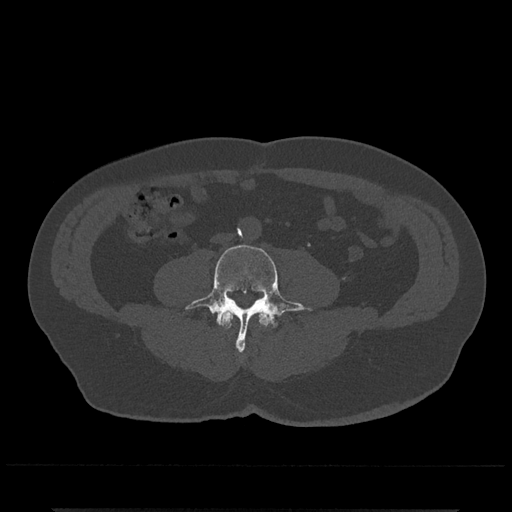
CT including the spine, one axial slice. Position 160 of 797 along the scan axis. 120 kVp. Bone window (W 1800 / L 400 HU). 0.5 mm slice thickness. 512 × 512 image matrix, field of view 393 × 393 mm. Male patient, age 67 years. Case-level facts recorded for this patient, not image findings: primary cancer: prostate.
Outlined on this slice (semi-automatic segmentation, software-assisted and operator-edited):
- L3 vertebra: bounding box [x1, y1, x2, y2] px = [220, 310, 270, 328]
- L4 vertebra: [185, 244, 315, 352]